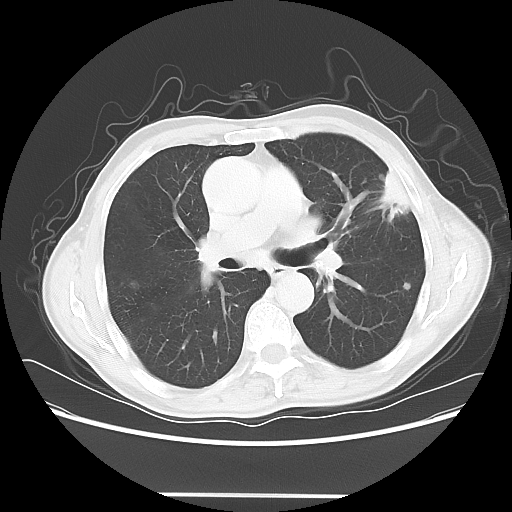
Chest CT, one axial slice; position 37 of 64 along the scan axis; lung window (W 1500 / L -600 HU); 512 × 512 image matrix. Patient: male, 71 years. Case-level facts recorded for this patient, not image findings: clinical TNM (as recorded): T1c N0 M0.
Outlined on this slice (rectangle marked by the reading radiologist):
- lung tumour (recorded histology: adenocarcinoma): bounding box [x1, y1, x2, y2] px = [379, 170, 416, 224]